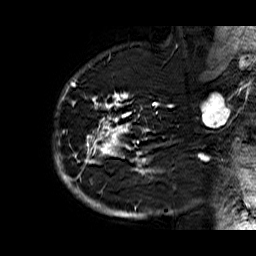
Breast MRI (dynamic contrast-enhanced), one sagittal slice; slice 48 of 60 in the series (ordered by position); dynamic contrast-enhanced series, time point 2 of 6 at this slice position (early post-contrast); 1.5 T; TE 6.3 ms, TR 32.9 ms; 256 × 256 image matrix. Female patient. Case-level facts recorded for this patient, not image findings: setting: breast cancer imaged before/during neoadjuvant chemotherapy; receptor status: HR-positive, HER2-negative.
Structures marked on this image (semi-automatic segmentation, software-assisted and operator-edited):
- analysis volume of interest (the breast-tissue region the enhancement analysis was run in; not a lesion): box from (x=54, y=74) to (x=176, y=210) px
- tumour enhancement mask (voxels above the 100 % enhancement threshold inside the analysis volume of interest): (x=55, y=75)–(x=173, y=210)